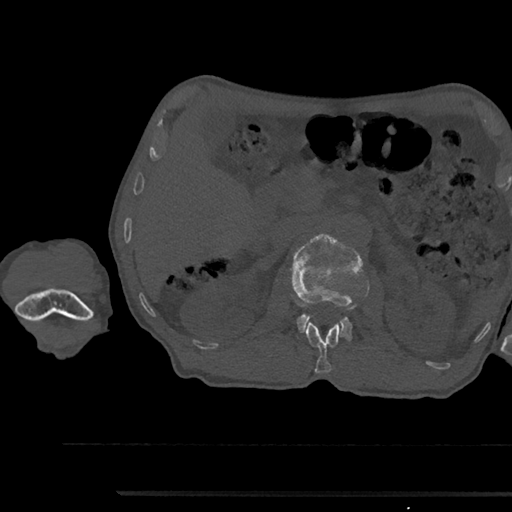
CT including the spine, one axial slice. 120 kVp. Bone window (W 1800 / L 400 HU). 0.5 mm slice thickness. 512 × 512 image matrix. Male patient, age 79 years. Case-level facts recorded for this patient, not image findings: primary cancer: prostate.
Structures marked on this image (semi-automatically segmented with operator editing):
- L1 vertebra: box from (x=305, y=322) to (x=339, y=373) px
- L2 vertebra: (x=291, y=235)–(x=363, y=341)